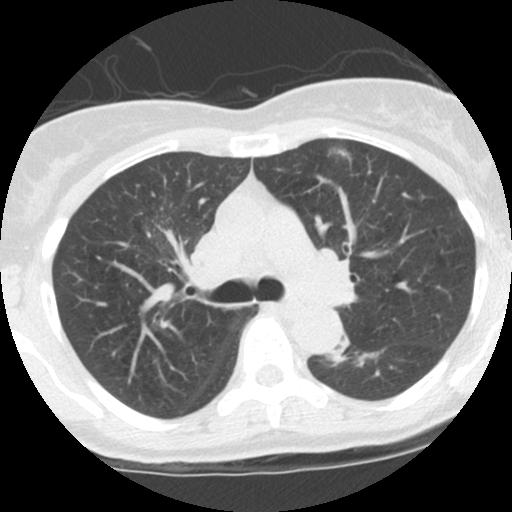
Low-dose screening chest CT, one axial slice. Position 72 of 115 along the scan axis. Reconstruction kernel STANDARD. 120 kVp. Lung window (W 1500 / L -600 HU). 2.5 mm slice thickness. 512 × 512 image matrix, field of view 290 × 290 mm.
Annotated regions visible in this slice (manually delineated by an expert):
- lesion 1 (tumor, lower lobe of left lung): box from (x=331, y=352) to (x=344, y=363) px